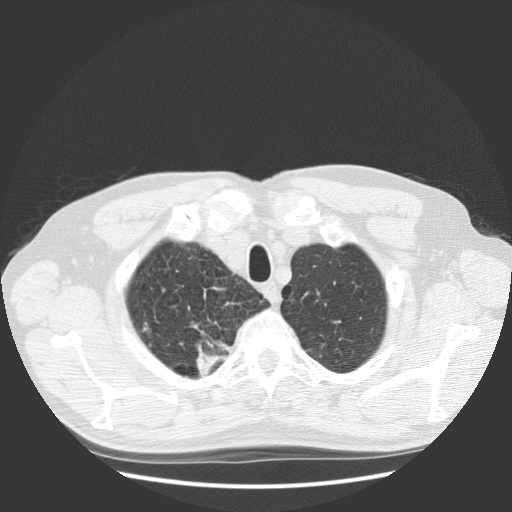
Low-dose screening chest CT, one axial slice; position 112 of 131 along the scan axis; reconstruction kernel STANDARD; 140 kVp; lung window (W 1500 / L -600 HU); 512 × 512 image matrix.
Structures marked on this image (outlined manually by an expert reader):
- lesion 1 (tumor, upper lobe of right lung): bounding box [x1, y1, x2, y2] px = [195, 333, 229, 376]